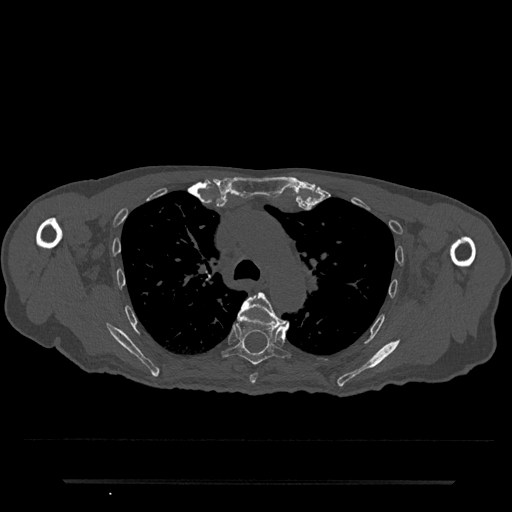
CT including the spine, one axial slice; position 543 of 797 along the scan axis; reconstruction kernel Br40s/3; bone window (W 1800 / L 400 HU); 0.5 mm slice thickness; 512 × 512 image matrix, field of view 427 × 427 mm. Patient: male, 74 years. From the clinical record (not read from this slice): primary cancer: prostate.
Outlined on this slice (semi-automatic segmentation, software-assisted and operator-edited):
- T5 vertebra: bounding box [x1, y1, x2, y2] px = [239, 292, 289, 384]
- T6 vertebra: [222, 307, 291, 365]